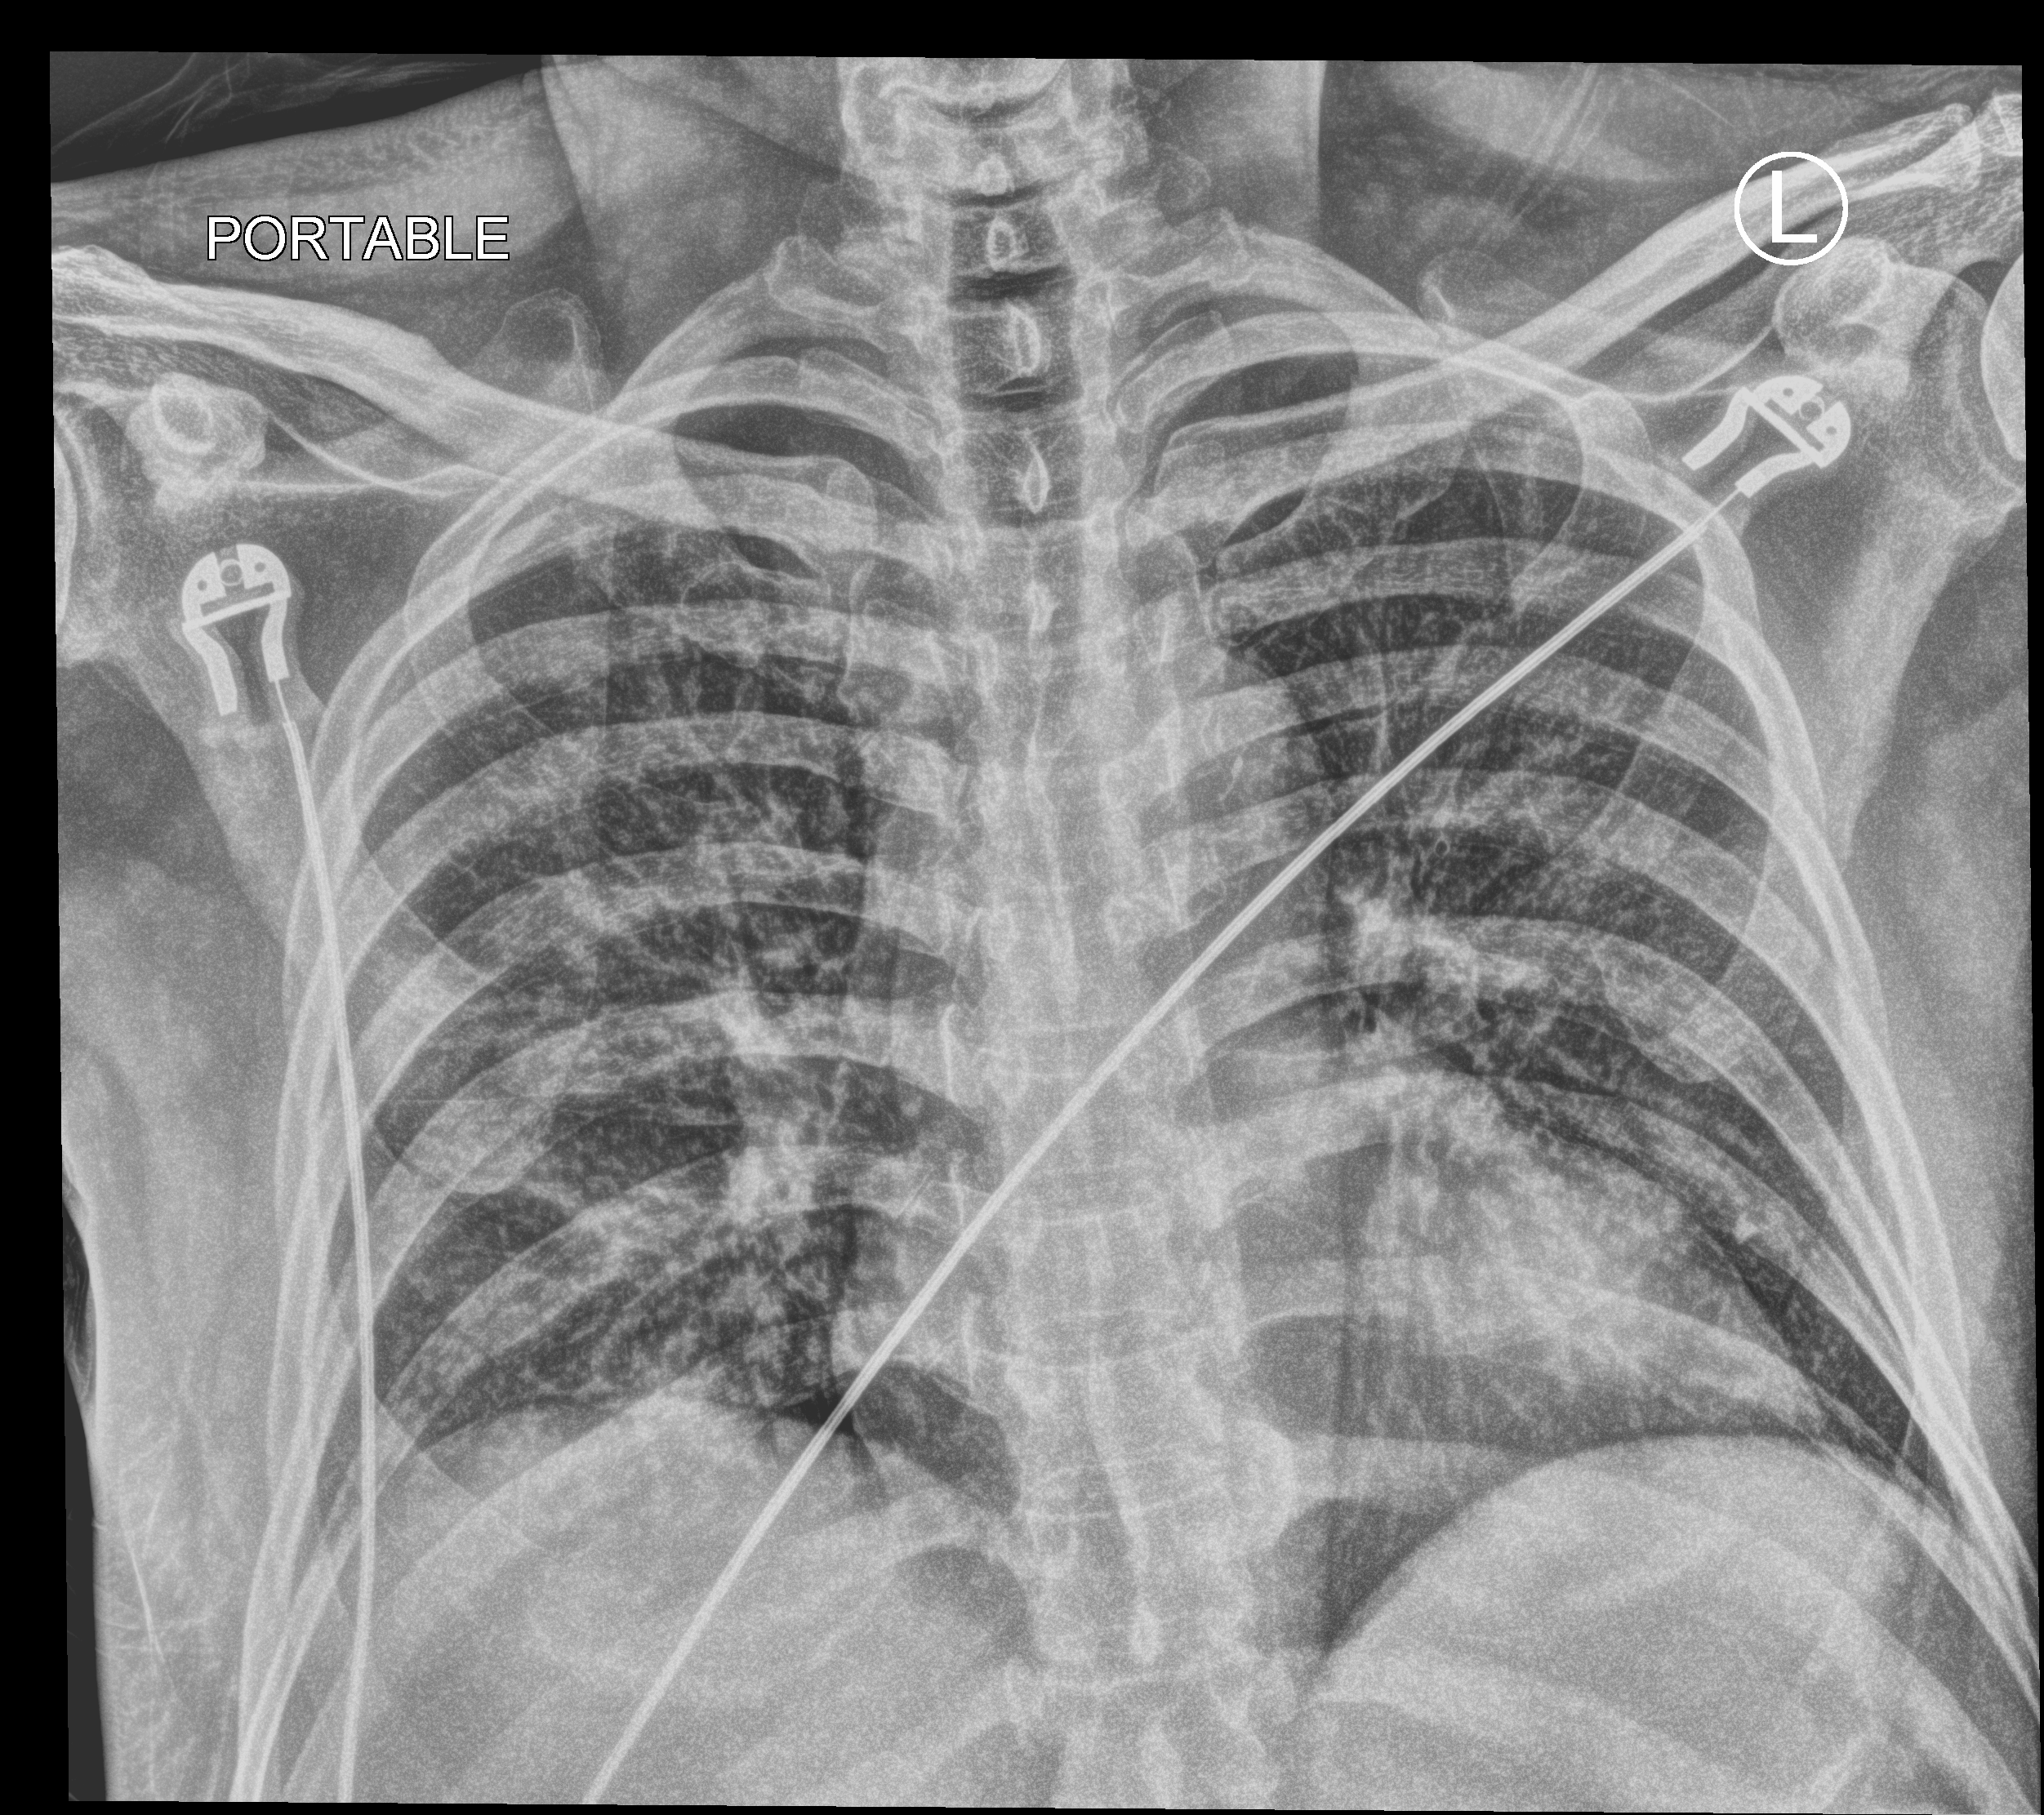
Bedside chest radiograph (computed radiography); anteroposterior (AP) projection. Male patient hospitalised with COVID-19, age 18–59 years.
Admission-level facts for this patient (not findings on this image; timing relative to this image not recorded): mechanically ventilated during this hospital stay: no; admitted to intensive care during this hospital stay: no.